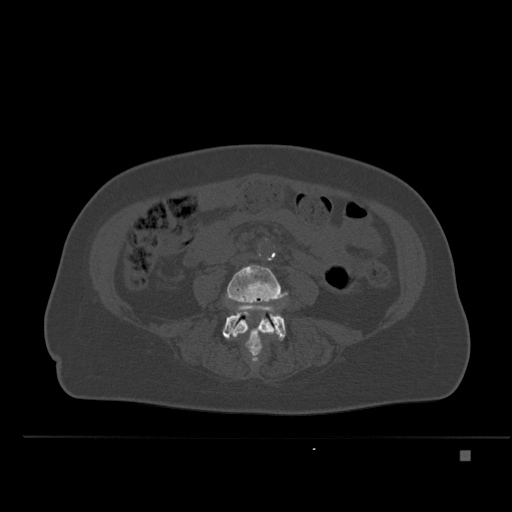
CT including the spine, one axial slice. Position 172 of 477 along the scan axis. Bone window (W 1800 / L 400 HU). 512 × 512 image matrix, field of view 422 × 422 mm. Patient: female, 74 years. From the clinical record (not read from this slice): primary cancer: colon.
Structures marked on this image (semi-automatically segmented with operator editing):
- L4 vertebra: bounding box [x1, y1, x2, y2] px = [227, 264, 285, 357]
- L5 vertebra: [222, 302, 286, 361]